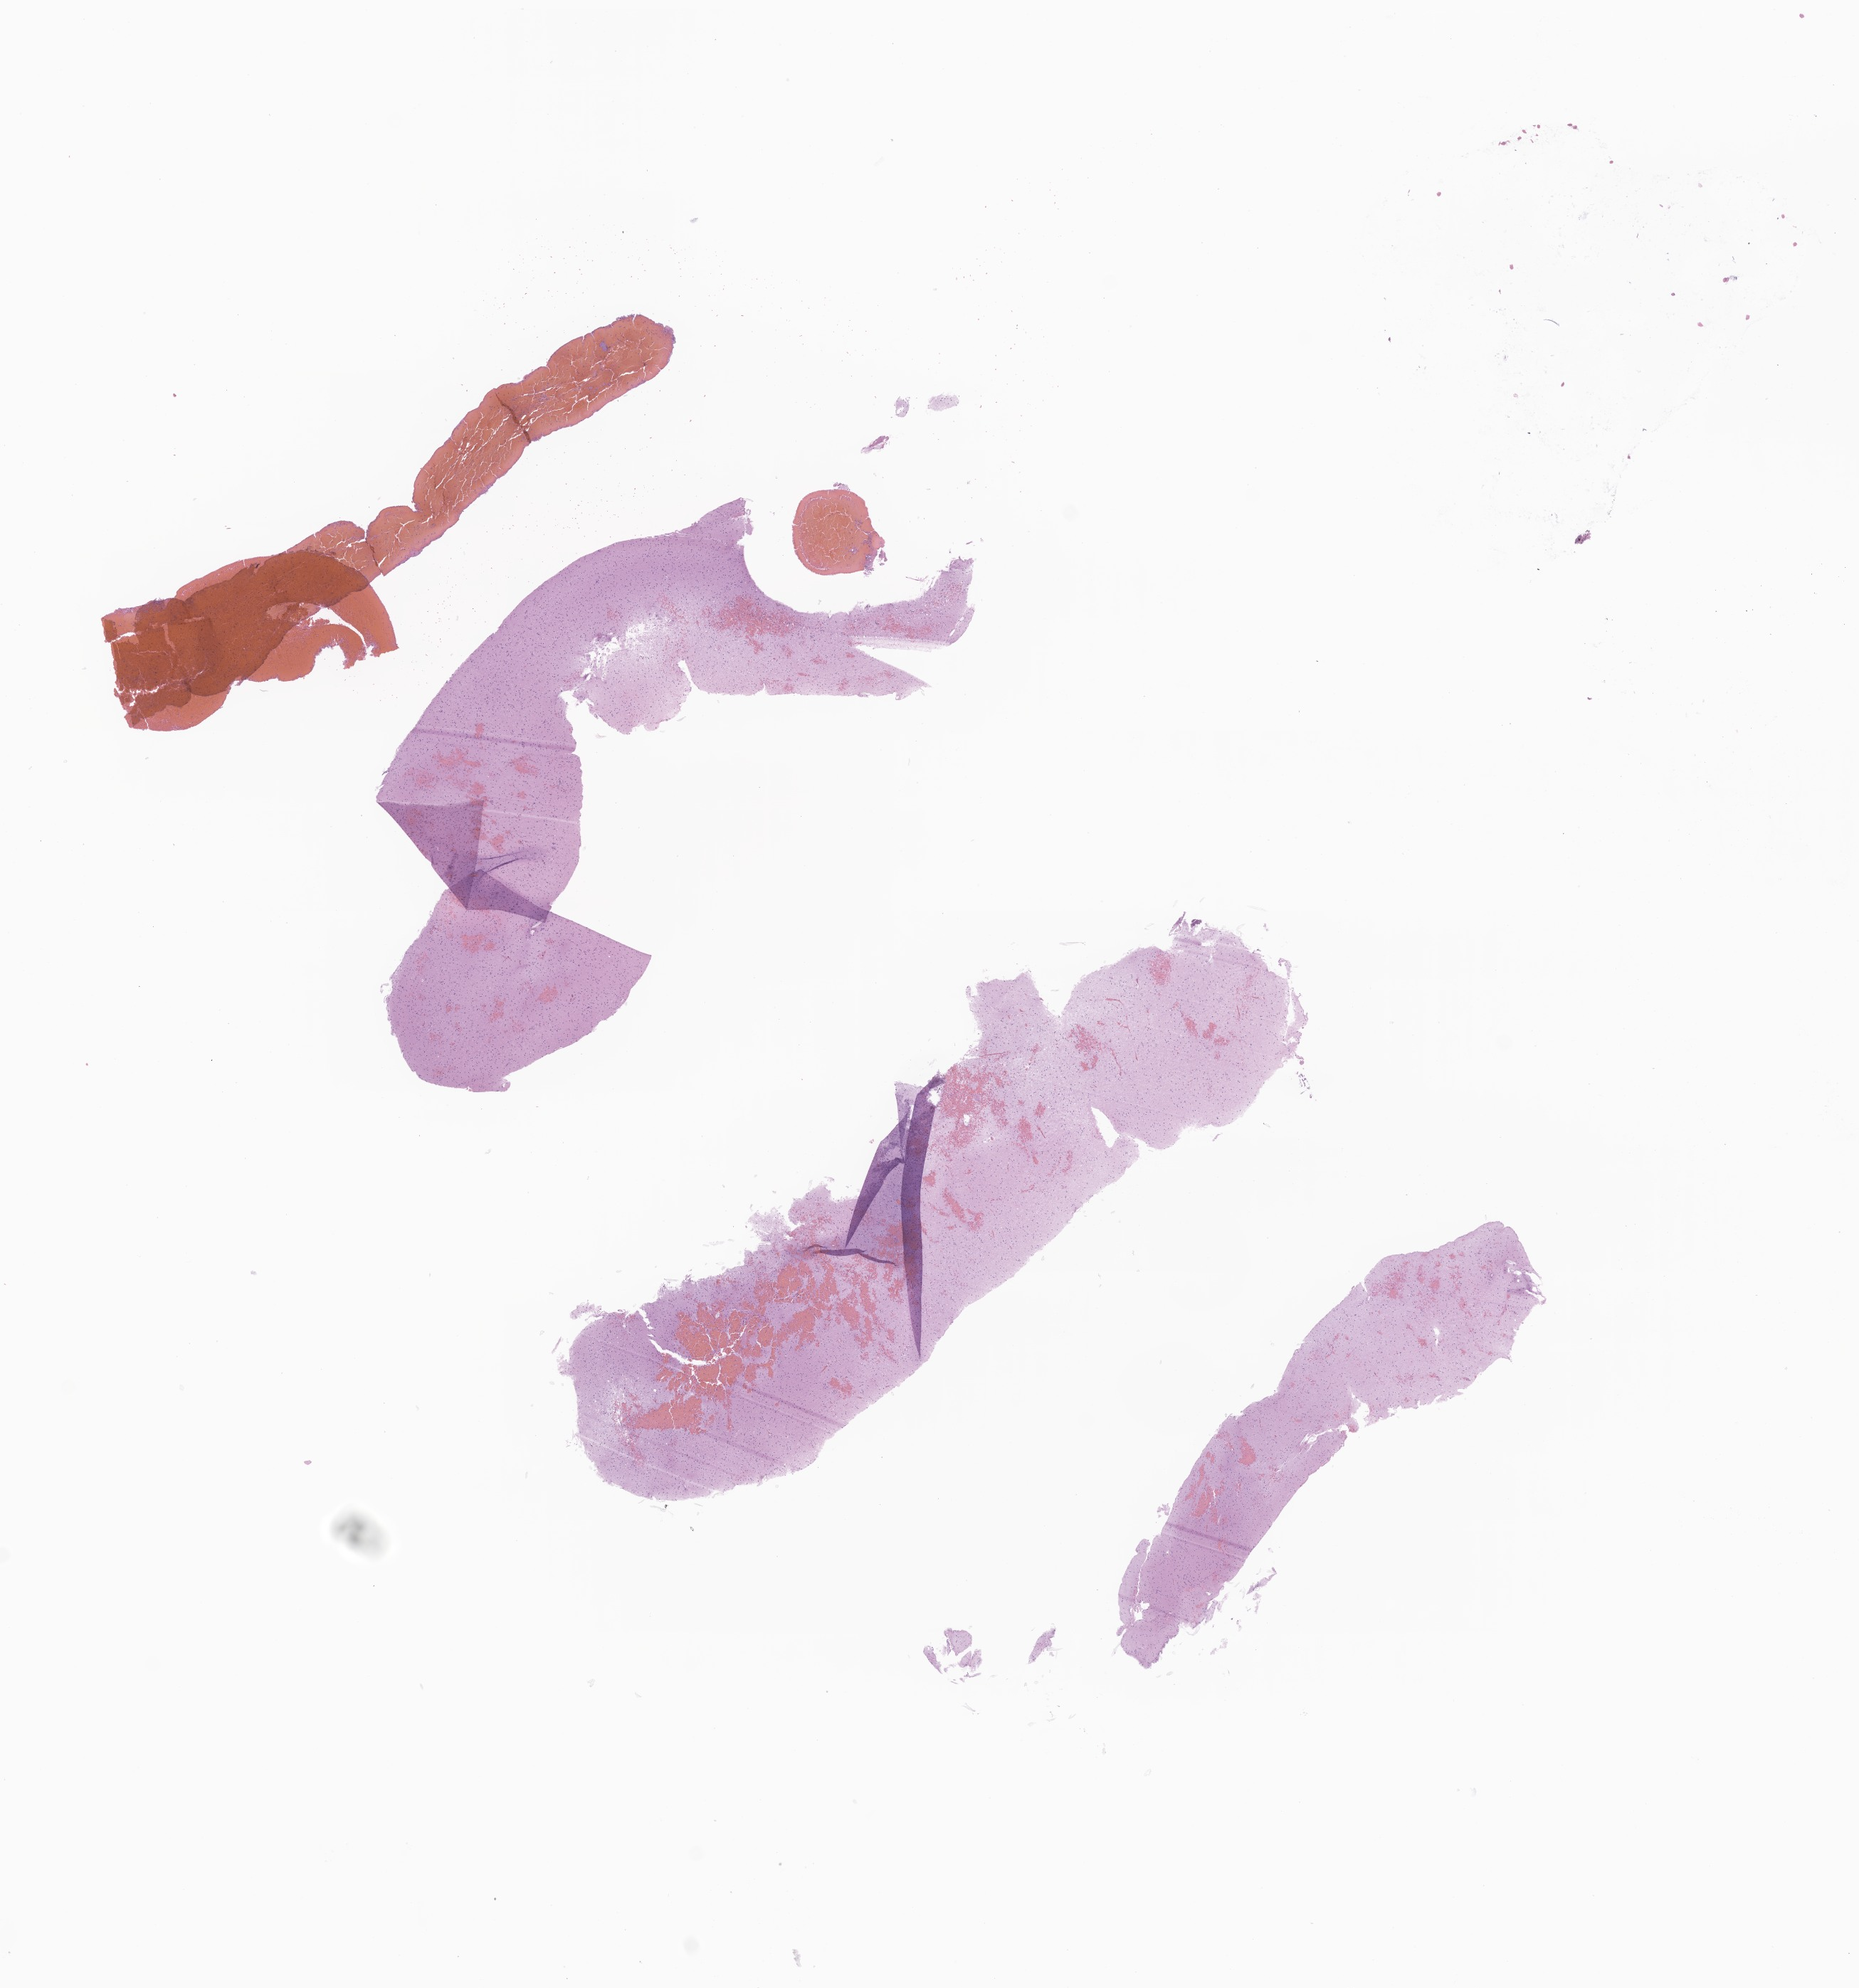
Digitized haematoxylin and eosin-stained section of tumor tissue from the brain — whole scanned area (about 11.0 x 11.8 mm) shown as a low-resolution overview, formalin-fixed, paraffin-embedded (FFPE) tissue. Female patient, age 216 months (18 years).
Recorded diagnosis: Astrocytoma, NOS.